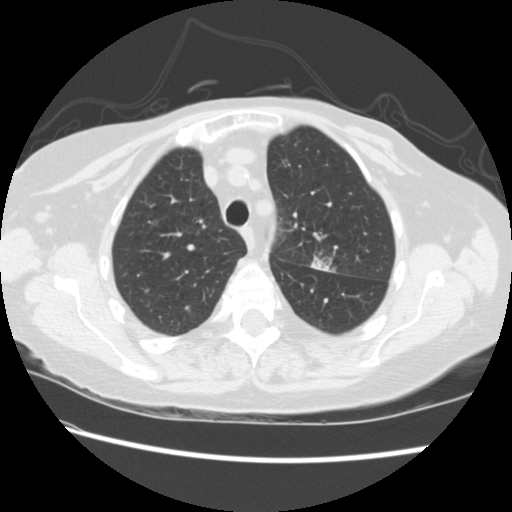
Axial slice from a low-dose chest CT screening exam; baseline annual screen; lung window (W 1500 / L -600 HU); standard (soft-tissue) reconstruction kernel (STANDARD); 120 kVp; slice 58 of 224 in the series; 512 × 512 image matrix, field of view 340 × 340 mm. Female participant, aged 74 years at enrolment. Former smoker at enrolment.
Lesion marked by an expert reader, bounding box (x1, y1, x2, y2) in pixels: (296, 235, 346, 279). The screening reader recorded 2 non-calcified nodules or masses ≥4 mm on this exam (left upper lobe, right lower lobe); which of them this box marks is not recorded. Official screen result: positive, change unspecified: nodule(s) >= 4 mm or enlarging nodule(s), mass(es), or other non-specific abnormalities suspicious for lung cancer.